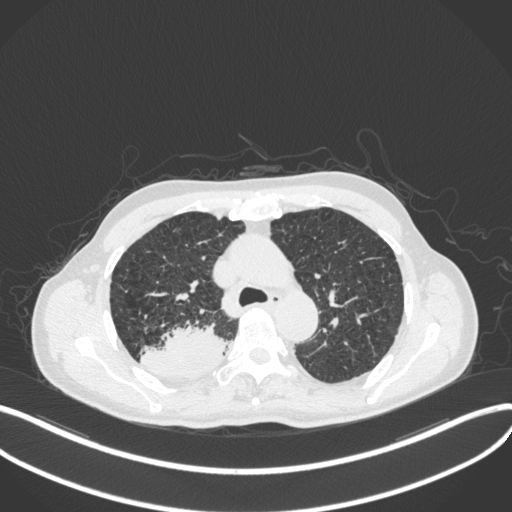
Chest CT, one axial slice; slice 319 of 423 in the series (ordered by position); reconstruction kernel B31f; lung window (W 1500 / L -600 HU); 1 mm slice thickness; 512 × 512 image matrix. Patient: male, 79 years. Case-level facts recorded for this patient, not image findings: clinical TNM (as recorded): T3 N0 M0.
Structures marked on this image (bounding box drawn by a radiologist):
- lung tumour (recorded histology: adenocarcinoma): bounding box (x1, y1, x2, y2) in pixels: (138, 320, 227, 379)